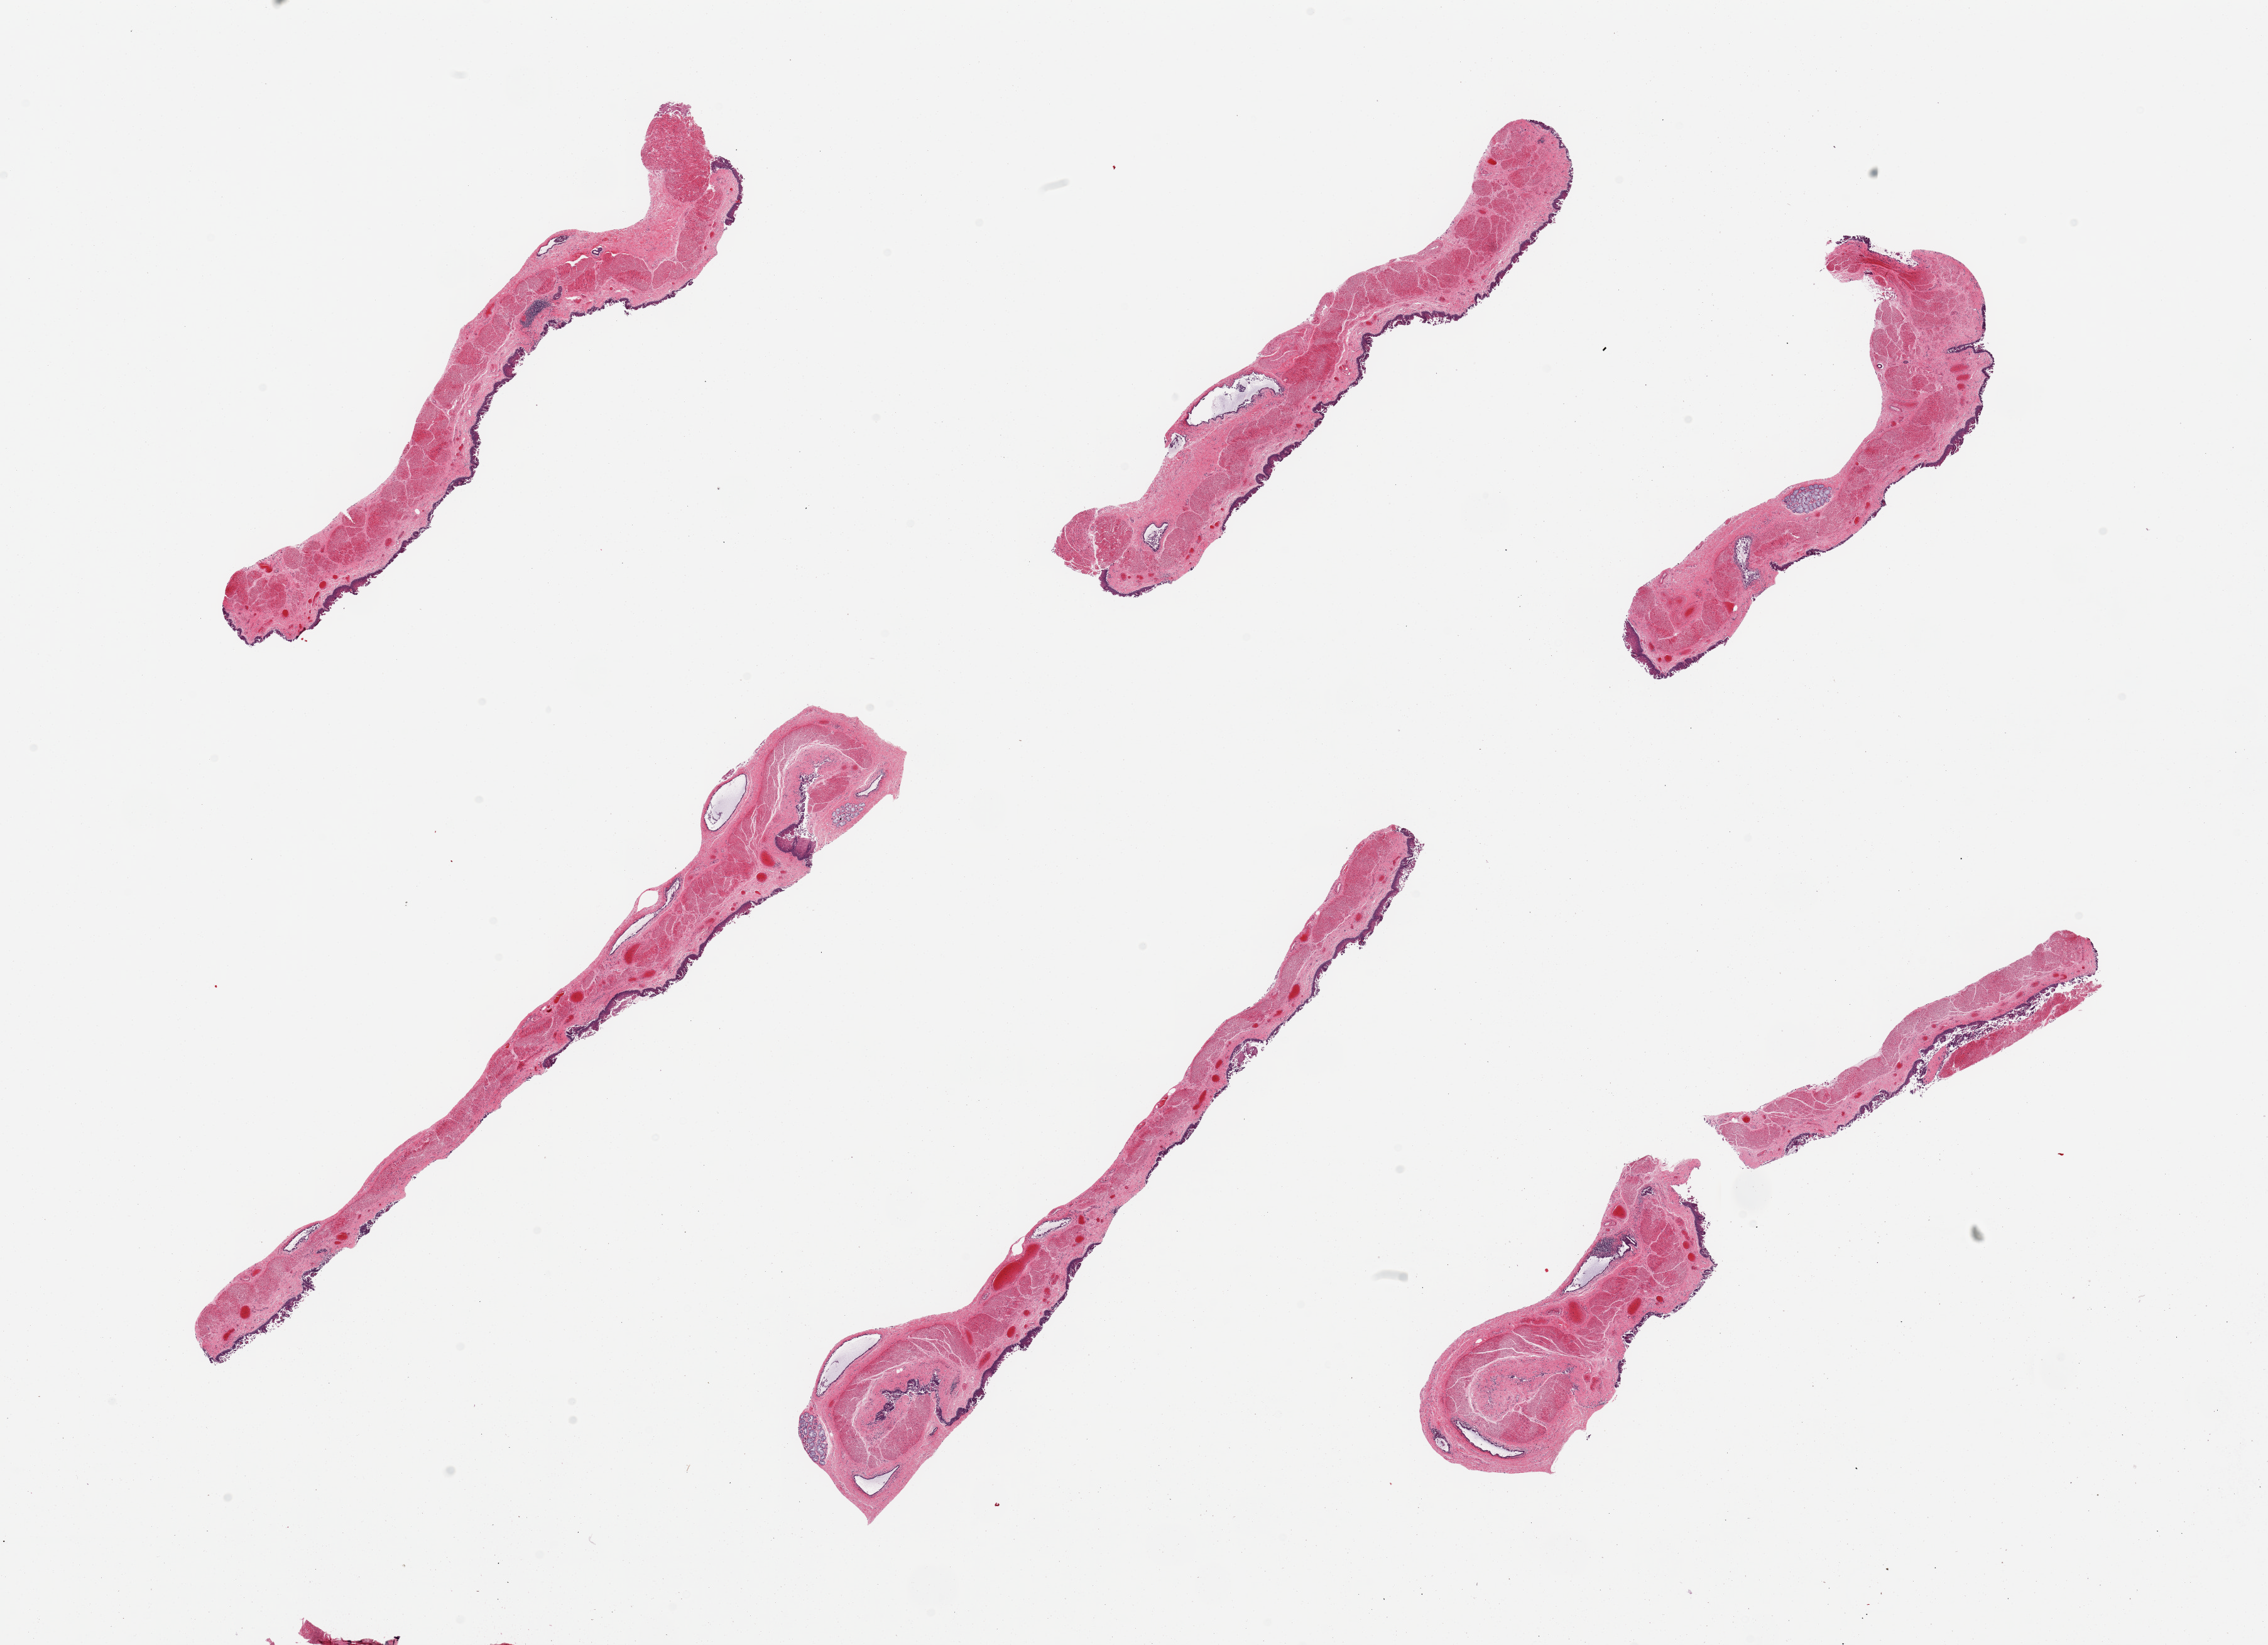
Digitized H&E-stained section — whole scanned area (about 28.5 x 20.7 mm) shown as a low-resolution overview; PAXgene-fixed, paraffin-embedded tissue; target tissue: esophageal mucous membrane; tissue donor sample. Donor sex: male.
• reviewer comment on this tissue sample: 6 pieces; considerable epithelial sloughing